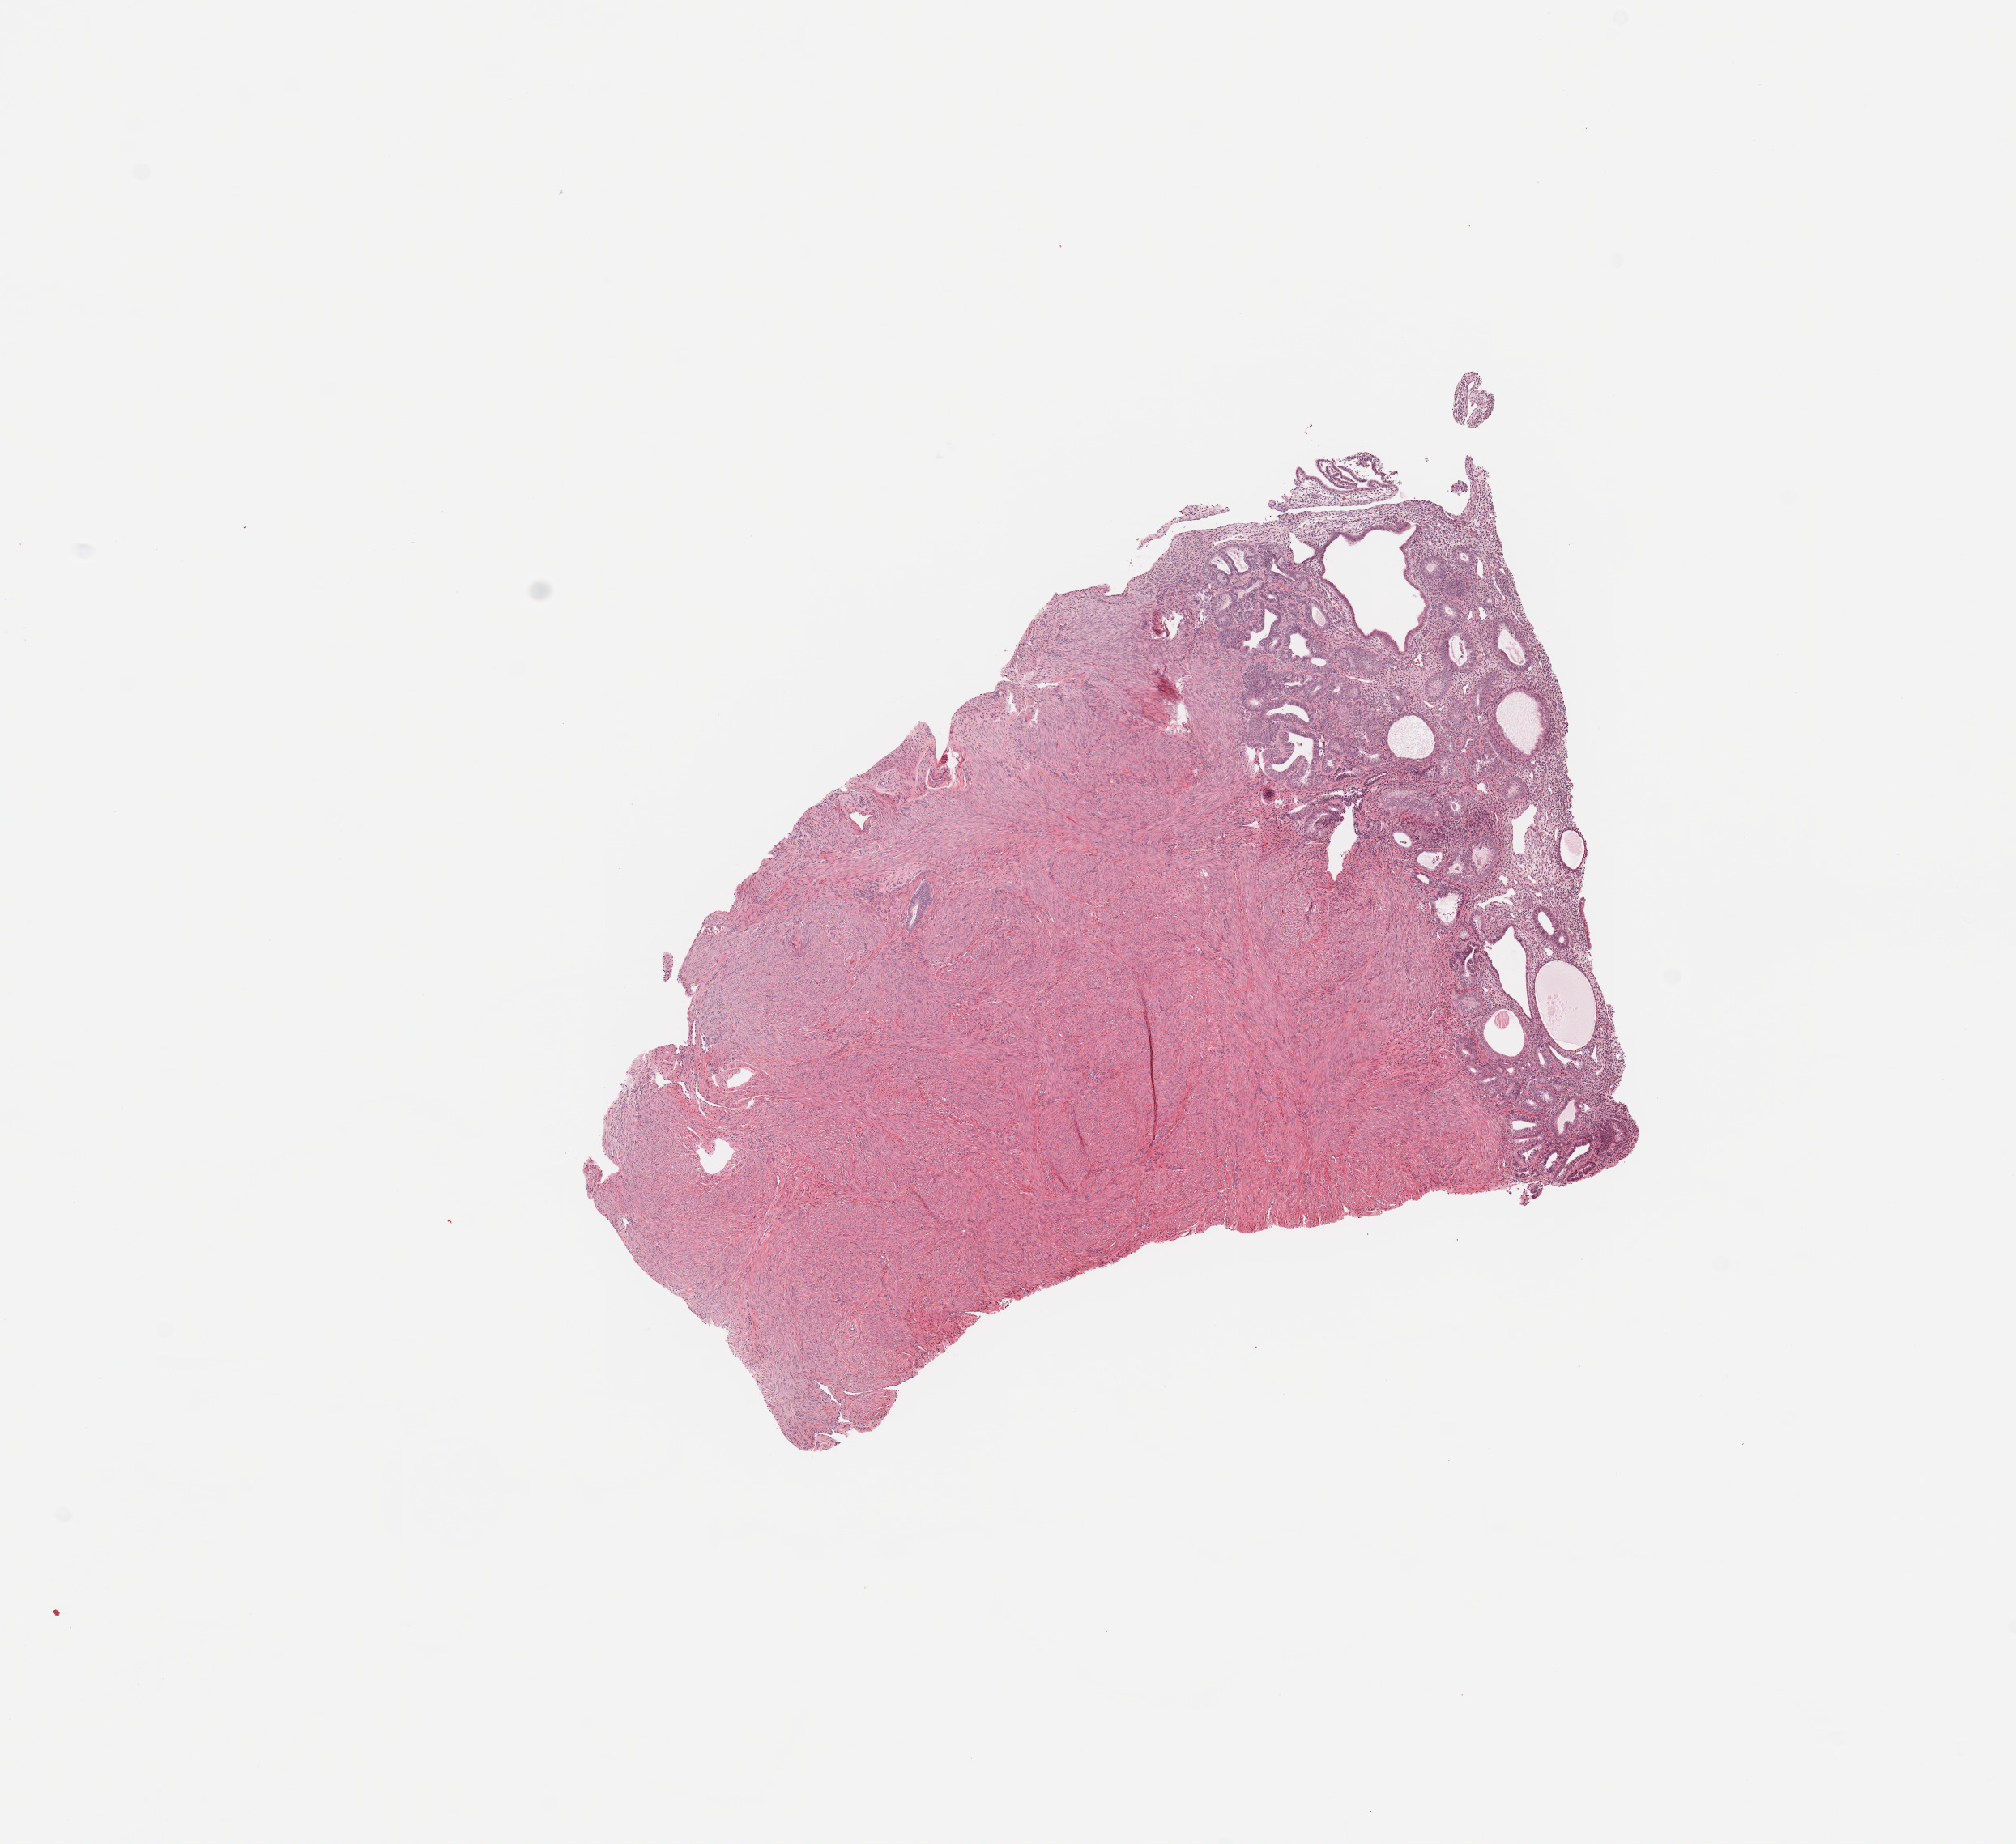
H&E whole-slide image, low-resolution overview of the scanned area, about 9.8 x 9.0 mm, normal (non-tumour) tissue sample, uterus. Female, 71 y/o.
This section: normal (non-tumour) tissue from the same patient. Patient diagnosis: Endometrioid adenocarcinoma, NOS.